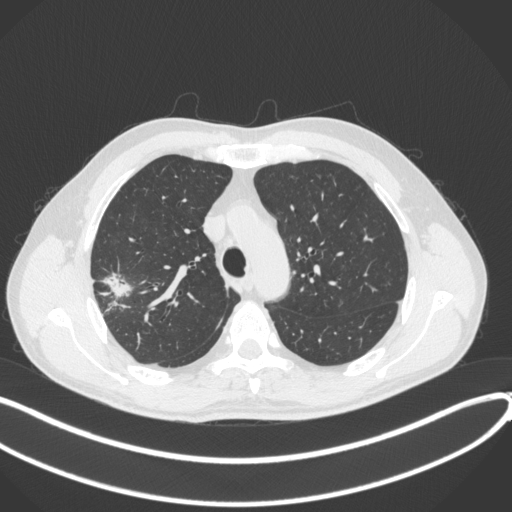
Chest CT, one axial slice; position 309 of 381 along the scan axis; reconstruction kernel B31f; lung window (W 1500 / L -600 HU); 512 × 512 image matrix, field of view 400 × 400 mm. Male patient, age 62 years. Case-level facts recorded for this patient, not image findings: clinical TNM (as recorded): T1c N0 M0; histopathological grade: G2-3.
Annotated regions visible in this slice (rectangle marked by the reading radiologist):
- lung tumour (recorded histology: adenocarcinoma): bounding box [x1, y1, x2, y2] px = [98, 265, 136, 301]